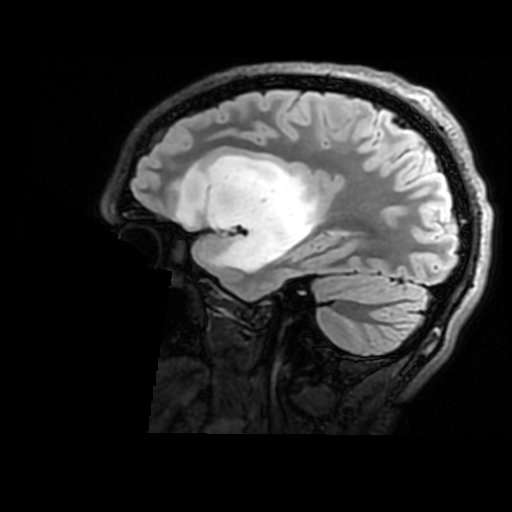
Brain MRI from a brain-tumour surgery series, one sagittal slice. Position 122 of 176 along the scan axis. T2 FLAIR. 1 mm slice thickness. 512 × 512 image matrix, field of view 240 × 240 mm. Case-level facts recorded for this patient, not image findings: histopathology: Astrocytoma; WHO grade: 2; IDH mutation: yes; tumour location: Right Insular.
Structures marked on this image (outlined manually by an expert reader):
- tumour: bounding box [x1, y1, x2, y2] px = [176, 154, 323, 275]